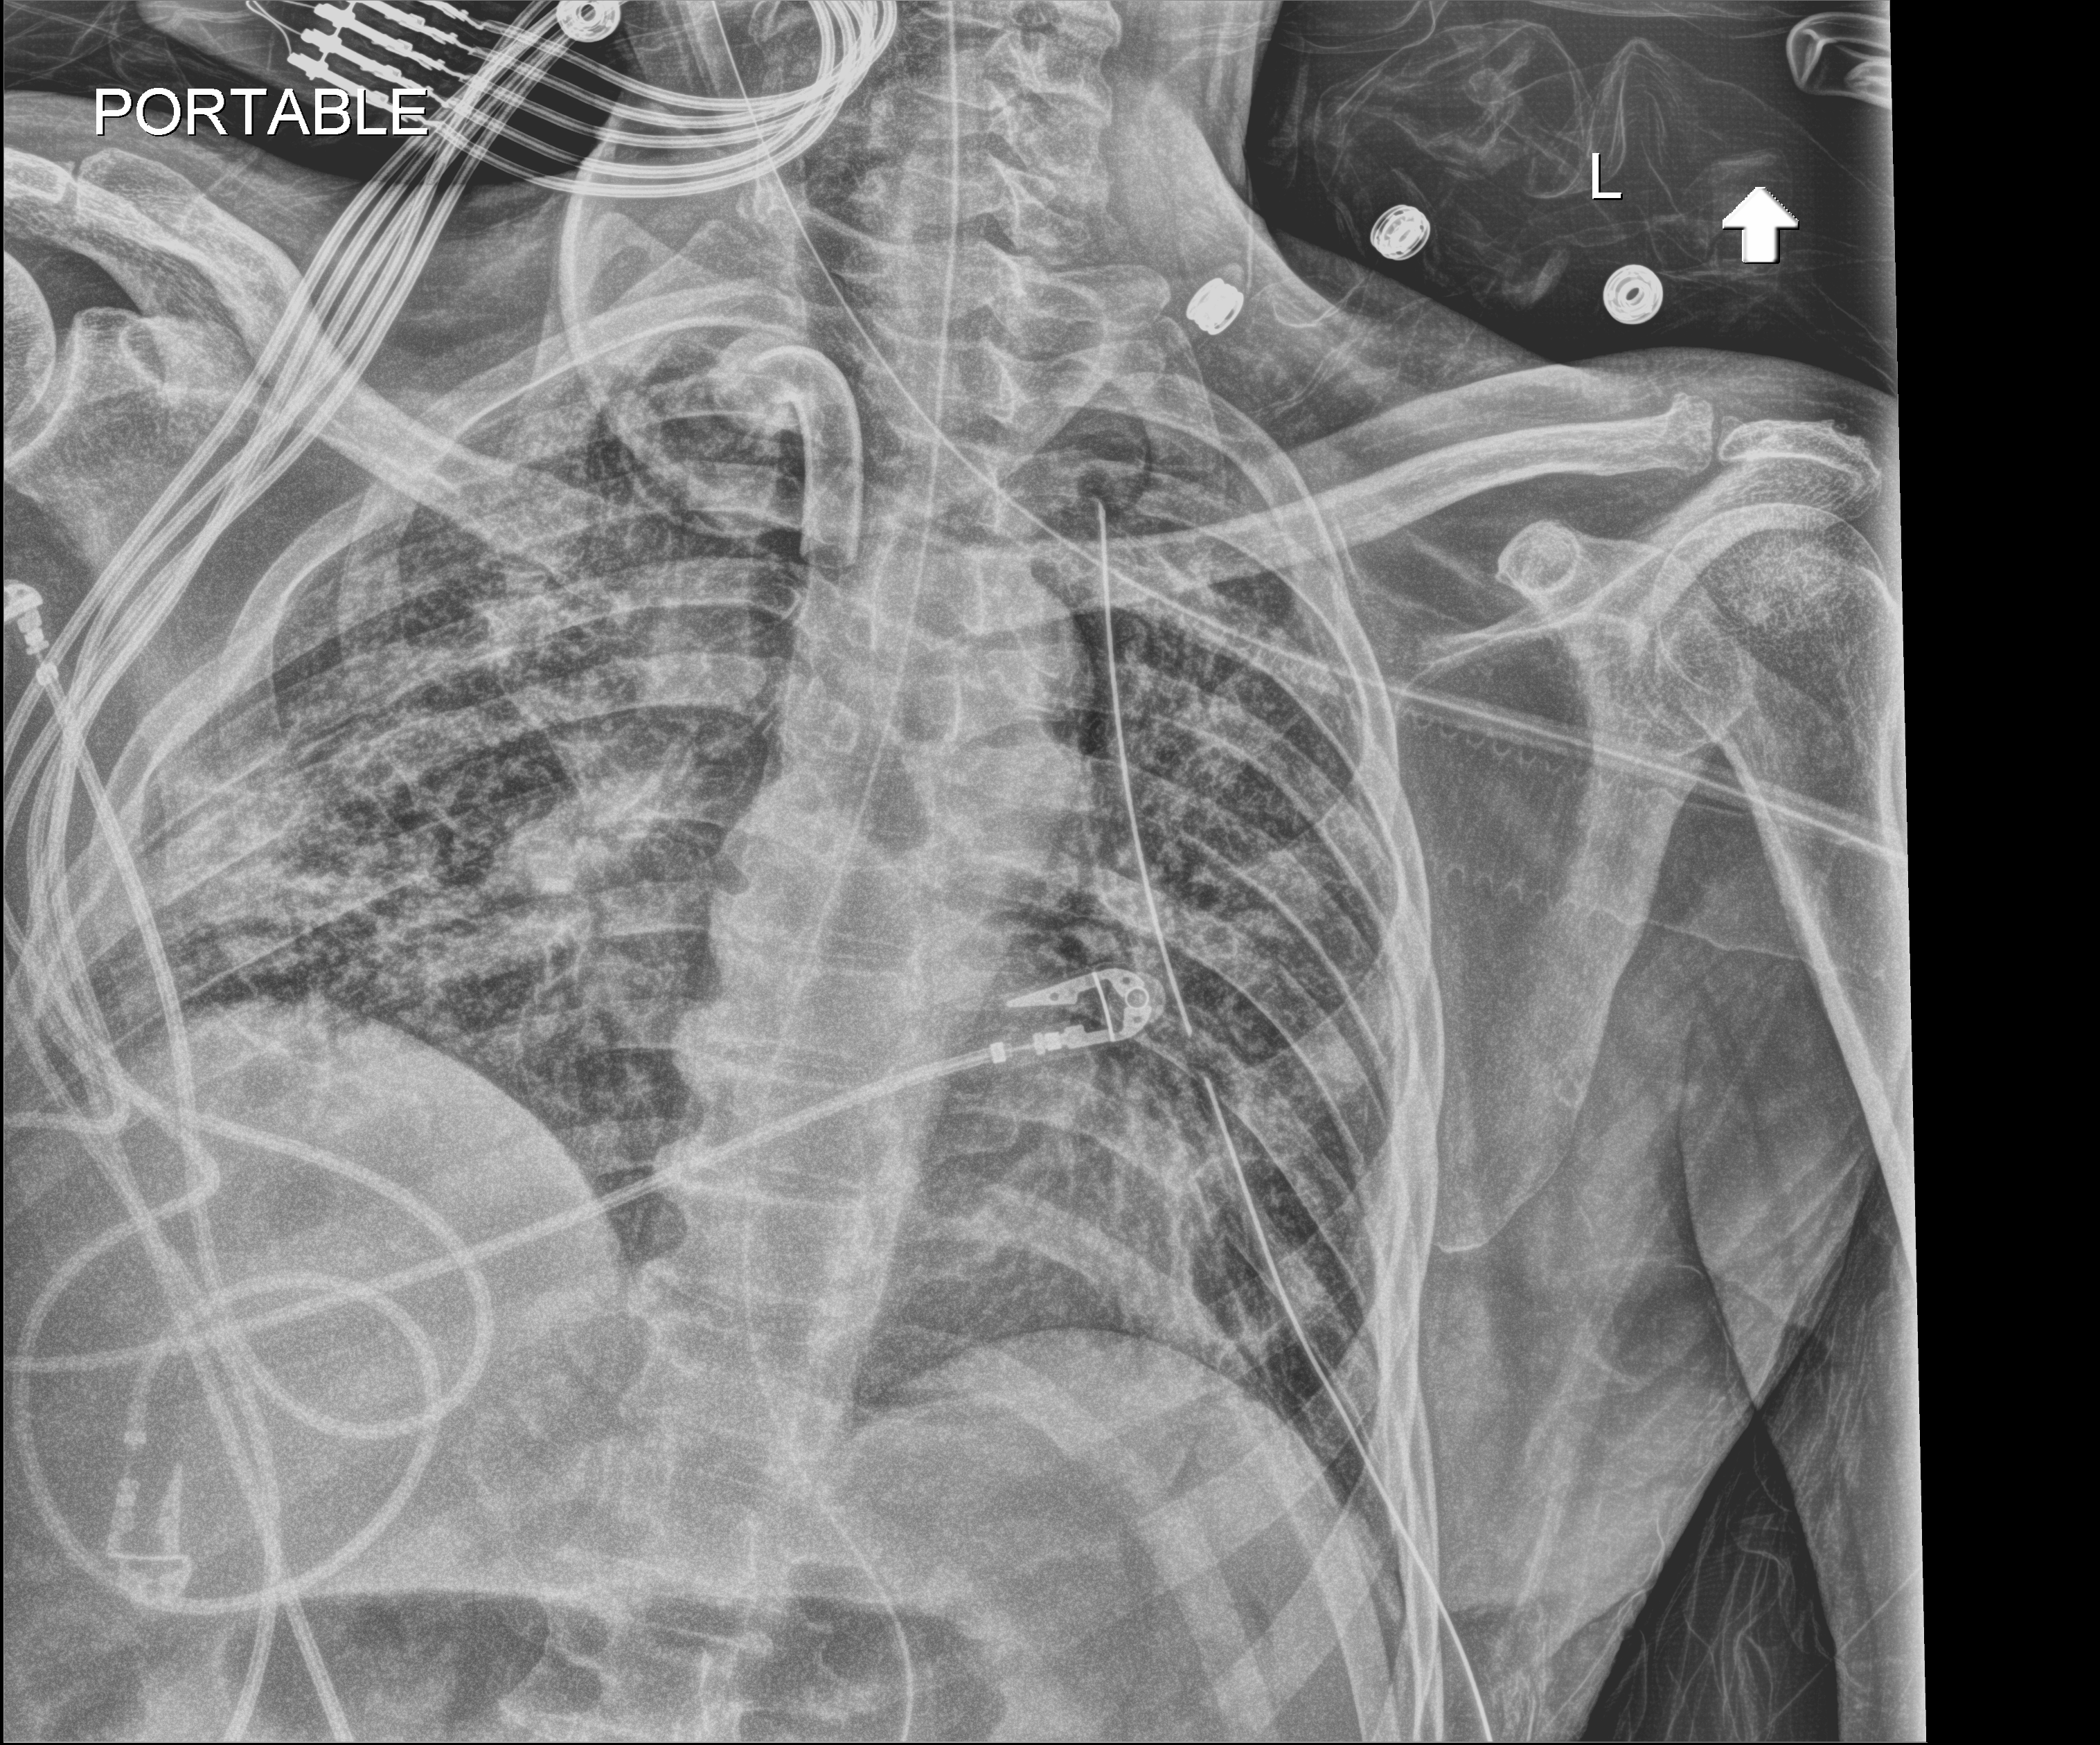
Chest X-ray; anteroposterior (AP) projection. Patient hospitalised with COVID-19; male, aged 18–59 years.
From the hospital-stay record, not from the radiograph (when in the stay this image was taken is not recorded): length of hospital stay: 83 days; mechanically ventilated during this hospital stay: yes; admitted to intensive care during this hospital stay: yes.